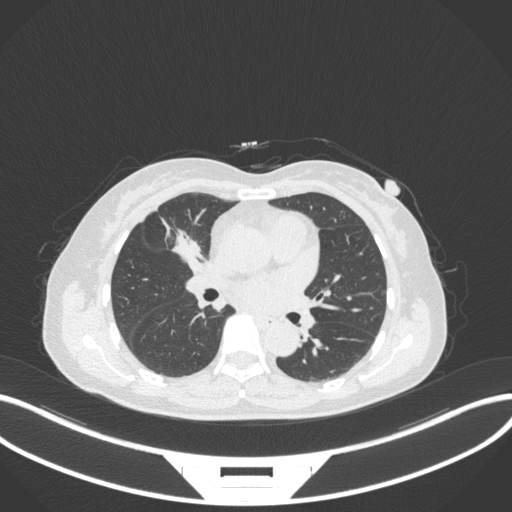
Chest CT, one axial slice. Reconstruction kernel B31f. 120 kVp. Lung window (W 1500 / L -600 HU). 512 × 512 image matrix. Female patient, age 51 years. From the clinical record (not read from this slice): clinical TNM (as recorded): T1c N0 M0; histopathological grade: G2.
Structures marked on this image (bounding box drawn by a radiologist):
- lung tumour (recorded histology: adenocarcinoma): bounding box <169,225,205,263> (left, top, right, bottom; pixels)